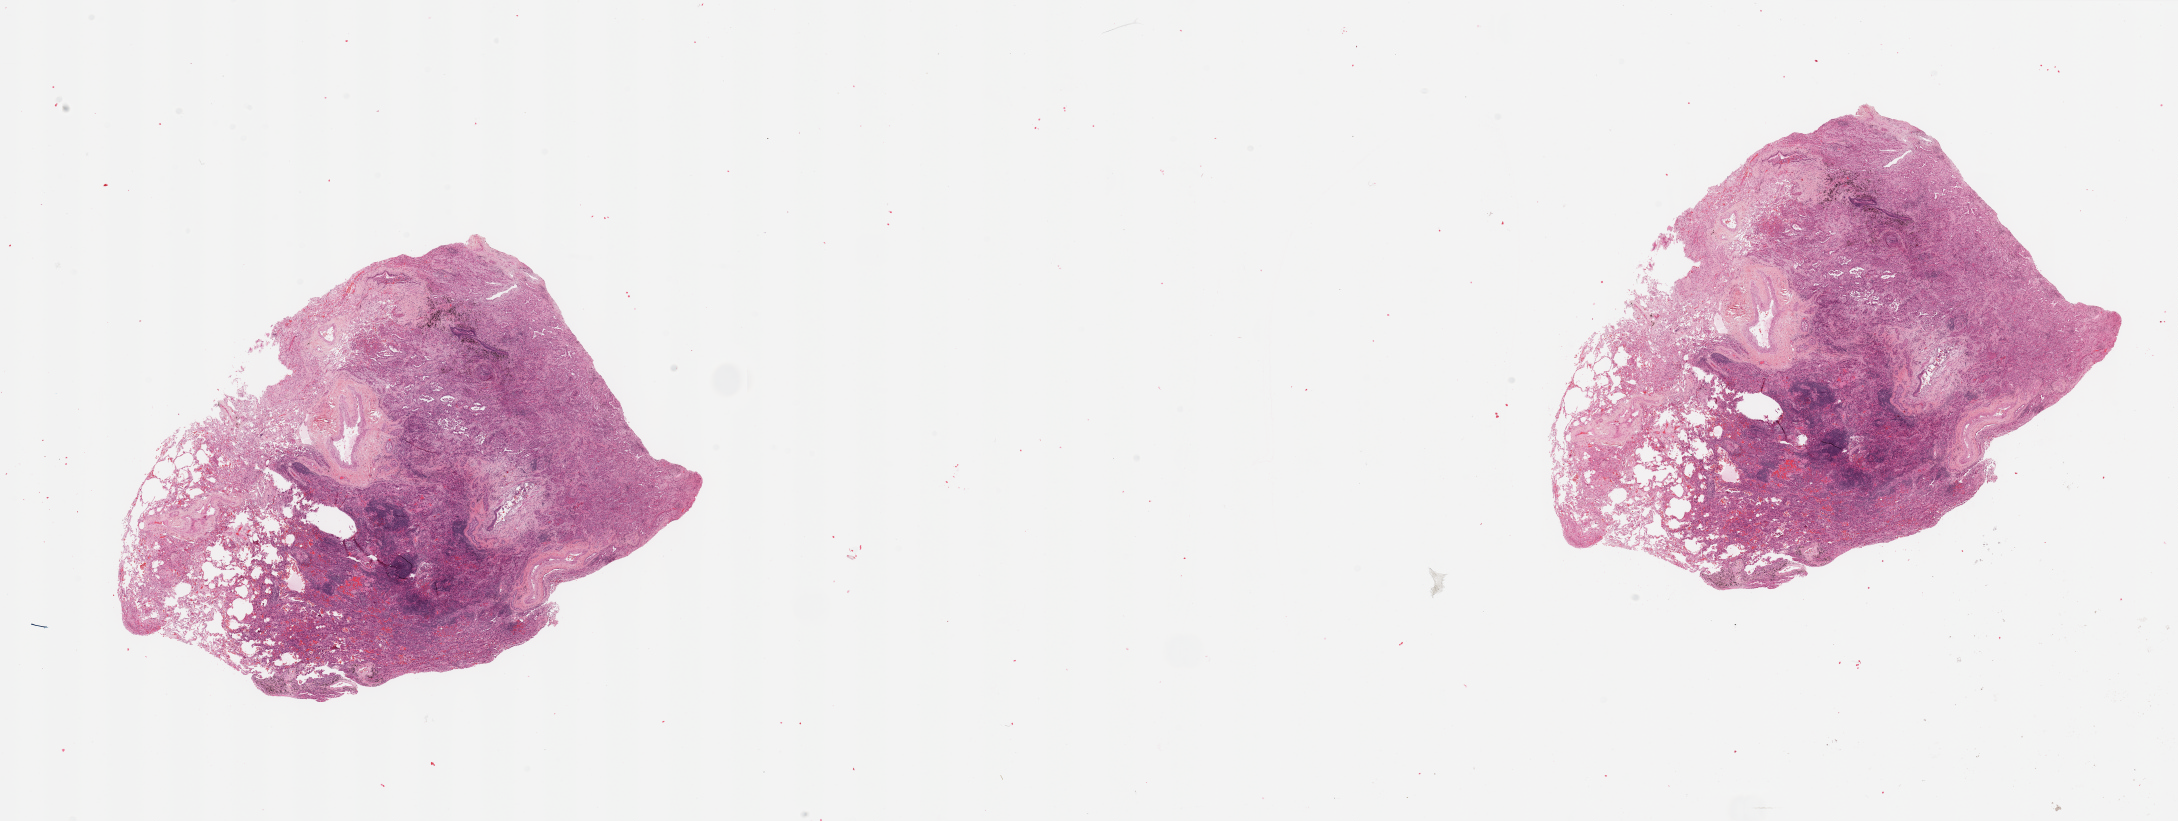
Hematoxylin and eosin (H&E) stained whole-slide image — shown as a low-resolution overview of the whole scanned area (about 34.5 x 13.0 mm). Lung, tumour tissue. 69-year-old female patient.
Histologic diagnosis: Adenocarcinoma, NOS.